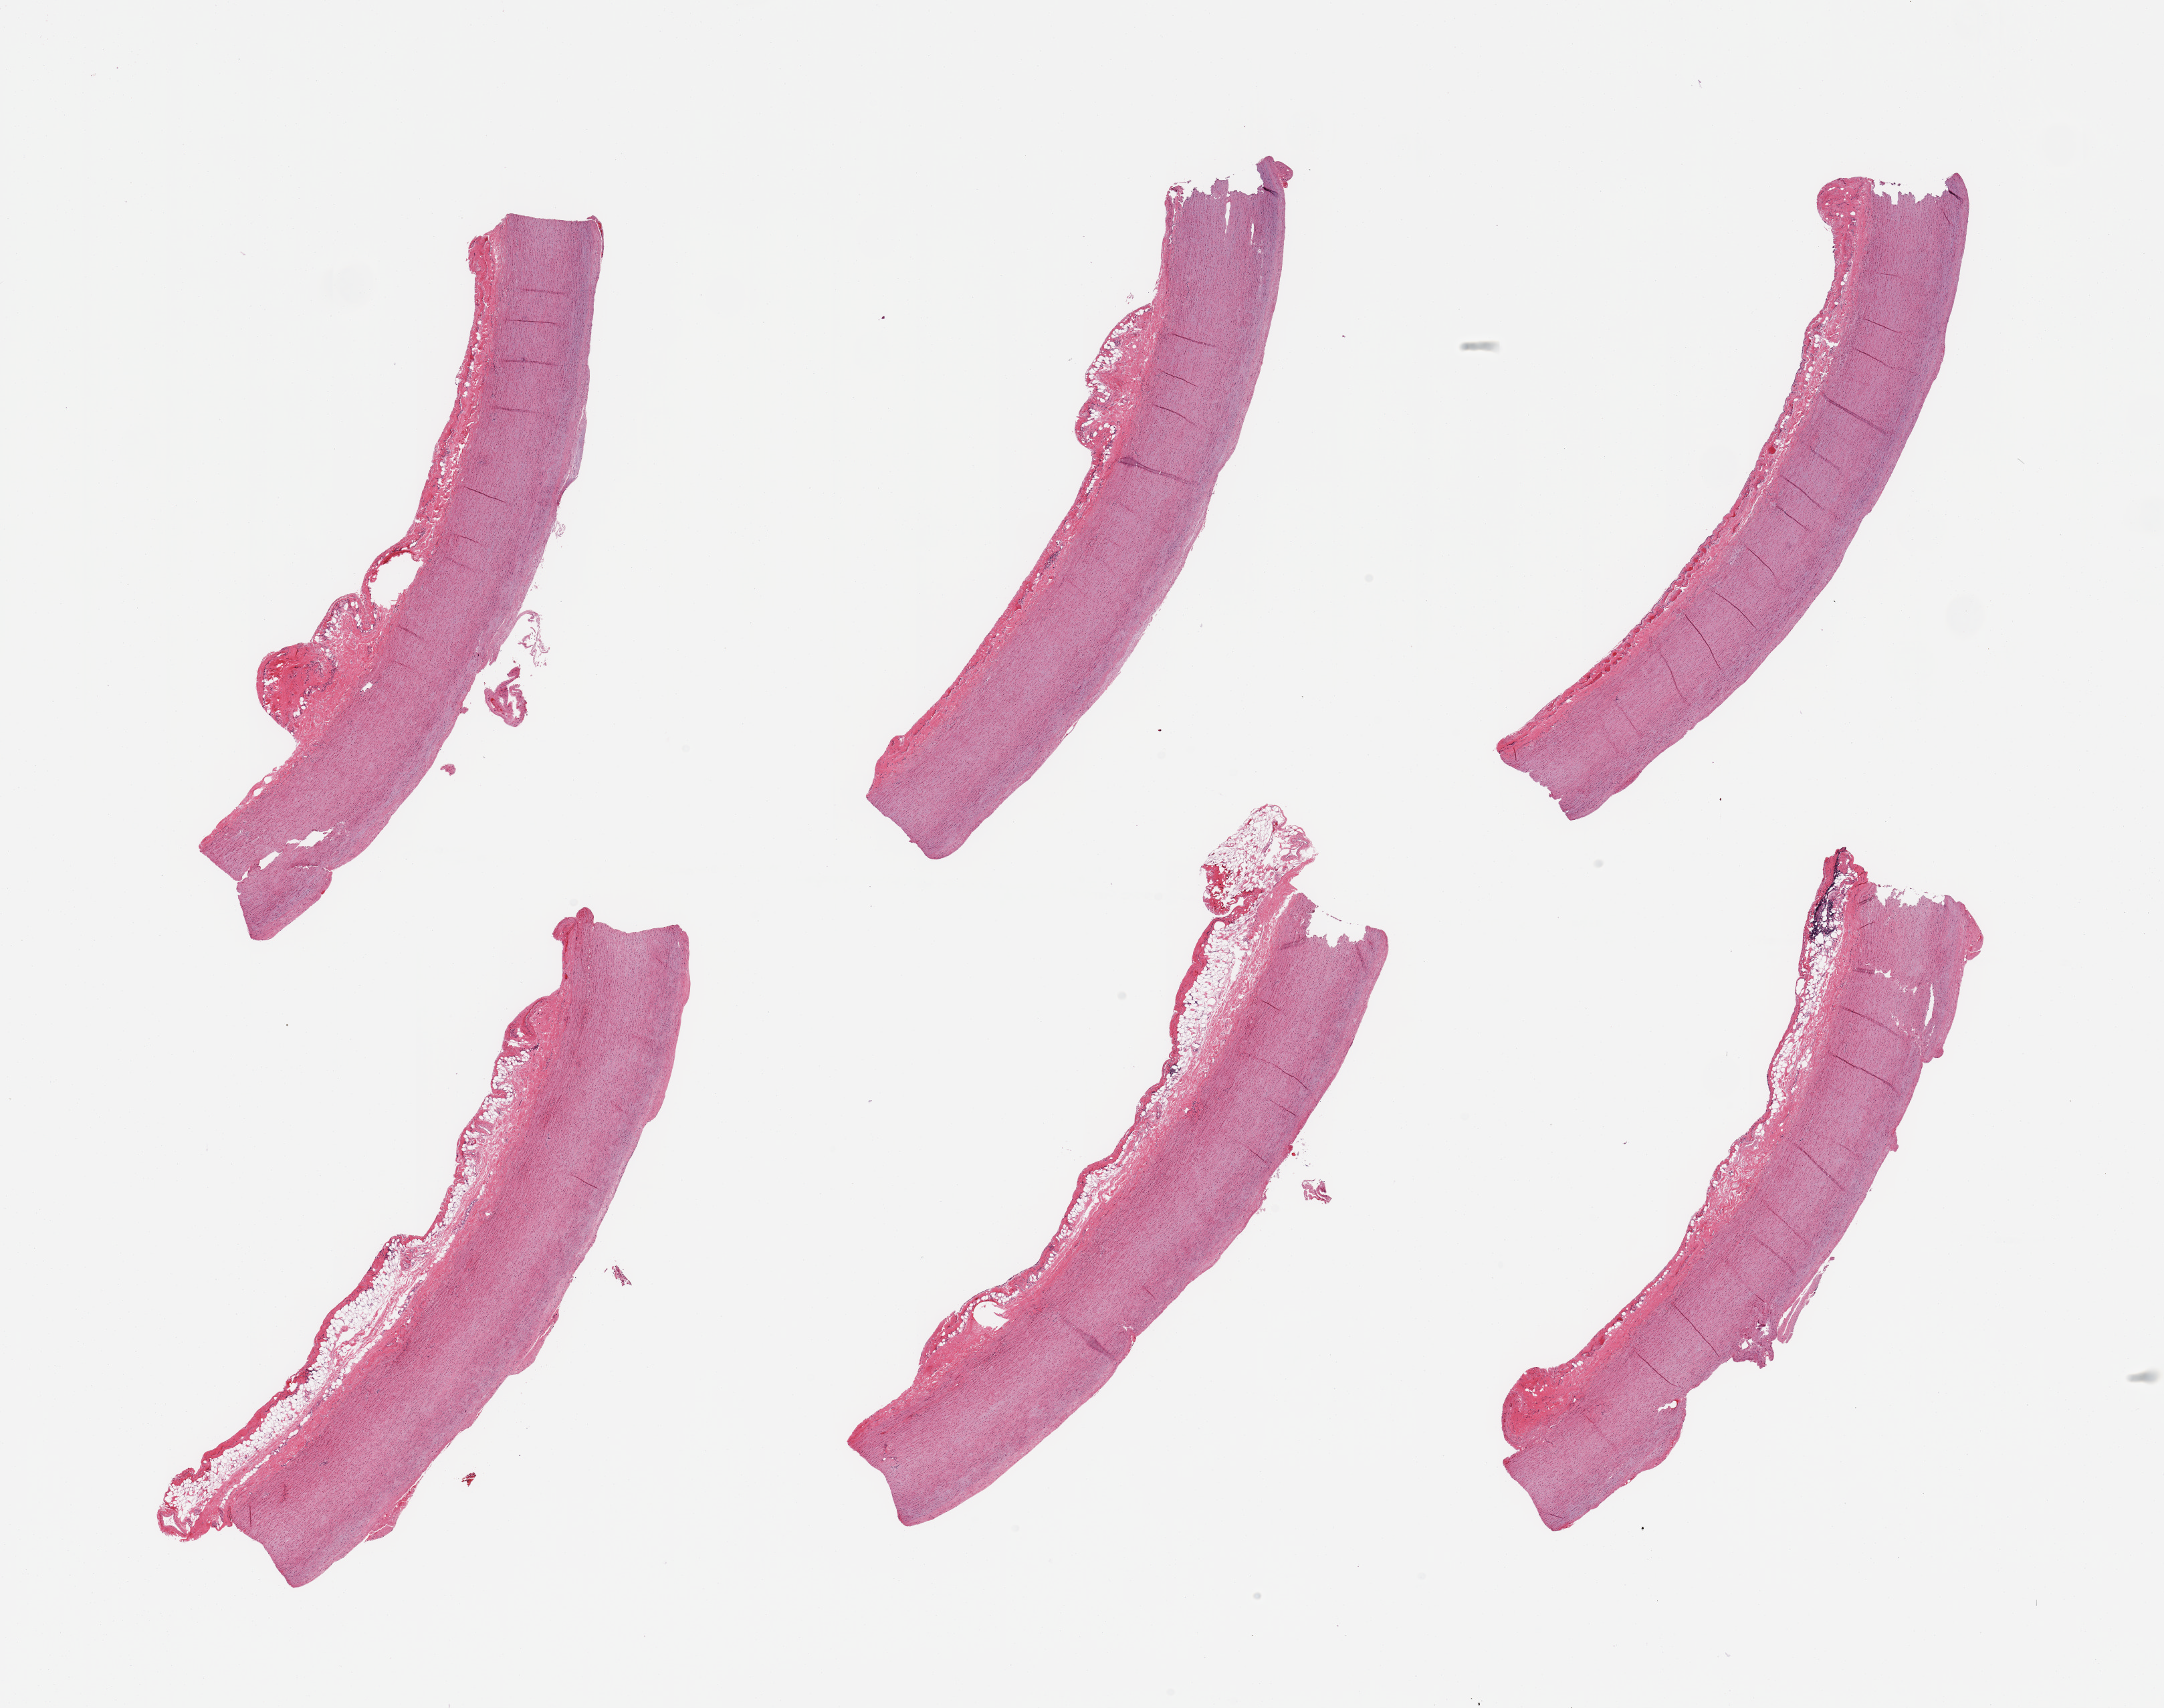
Digitized haematoxylin and eosin-stained section, whole scanned area (about 25.6 x 20.2 mm) shown as a low-resolution overview, PAXgene-fixed, paraffin-embedded tissue, target tissue: aorta, donor tissue sample. Donor sex: male.
Reviewer comment on this tissue sample: 6 pieces; slight flat plaques; adventitial fat up to 0.6mm thick.